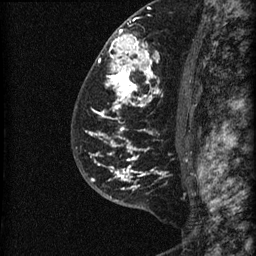
Breast MRI (dynamic contrast-enhanced), one sagittal slice. Slice 43 of 60 in the series (ordered by position). Dynamic contrast-enhanced series, image 2 of 3 at this slice position (ordered by acquisition). 1.5 T. TE 4.2 ms, TR 22.7 ms. 1.5 mm slice thickness. 256 × 256 image matrix, field of view 180 × 180 mm. Patient: female, 48 years. From the clinical record (not read from this slice): setting: breast cancer imaged before/during neoadjuvant chemotherapy; receptor status: triple-negative.
Annotated regions visible in this slice (semi-automatically segmented with operator editing):
- analysis volume of interest (the breast-tissue region the enhancement analysis was run in; not a lesion): box from (x=81, y=23) to (x=186, y=202) px
- tumour enhancement mask (voxels above the 90 % enhancement threshold inside the analysis volume of interest): (x=89, y=29)–(x=166, y=190)